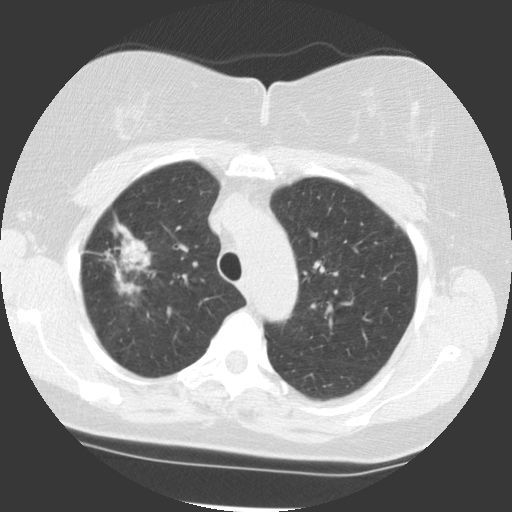
Low-dose screening chest CT, axial slice, baseline screening round, lung window (W 1500 / L -600 HU), 2.5 mm slice thickness, standard (soft-tissue) reconstruction kernel (STANDARD). Female, age 68 years at enrolment. Former smoker at enrolment.
Lesion marked by an expert reader, bounding box [x1, y1, x2, y2] px = [88, 235, 153, 293]. Screening reader's record for this exam (one nodule recorded; not confirmed to be the boxed lesion): non-calcified nodule or mass ≥4 mm, right upper lobe, 42 × 20 mm, spiculated (stellate) margins, soft tissue attenuation. Lung cancer was diagnosed 51 days after this screen: adenocarcinoma, NOS, right upper lobe, moderately differentiated (G2), stage IB (AJCC 6th edition), 31 mm at pathology.